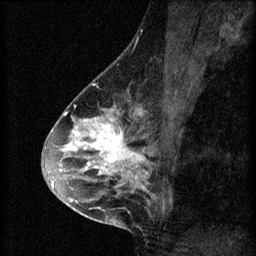
Breast MRI (dynamic contrast-enhanced), one sagittal slice. Slice 35 of 60 in the series (ordered by position). 3 images stored at this slice position (order not interpretable as contrast timing). 1.5 T. TE 4.2 ms, TR 8.2 ms. 256 × 256 image matrix. Female patient, age 45 years.
Structures marked on this image (semi-automatic segmentation, software-assisted and operator-edited):
- analysis volume of interest (the breast-tissue region the enhancement analysis was run in; not a lesion): box from (x=54, y=104) to (x=155, y=217) px
- tumour enhancement mask (voxels above the 70 % enhancement threshold inside the analysis volume of interest): (x=54, y=106)–(x=149, y=207)